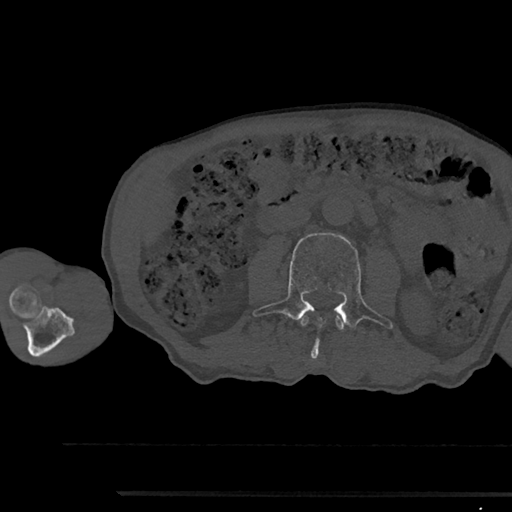
CT including the spine, one axial slice. Slice 502 of 797 in the series (ordered by position). 120 kVp. Bone window (W 1800 / L 400 HU). 0.5 mm slice thickness. 512 × 512 image matrix, field of view 367 × 367 mm. Male patient, age 79 years. From the clinical record (not read from this slice): primary cancer: prostate.
Structures marked on this image (semi-automatic segmentation, software-assisted and operator-edited):
- L2 vertebra: bounding box [x1, y1, x2, y2] px = [300, 316, 344, 330]
- L3 vertebra: [253, 233, 393, 359]